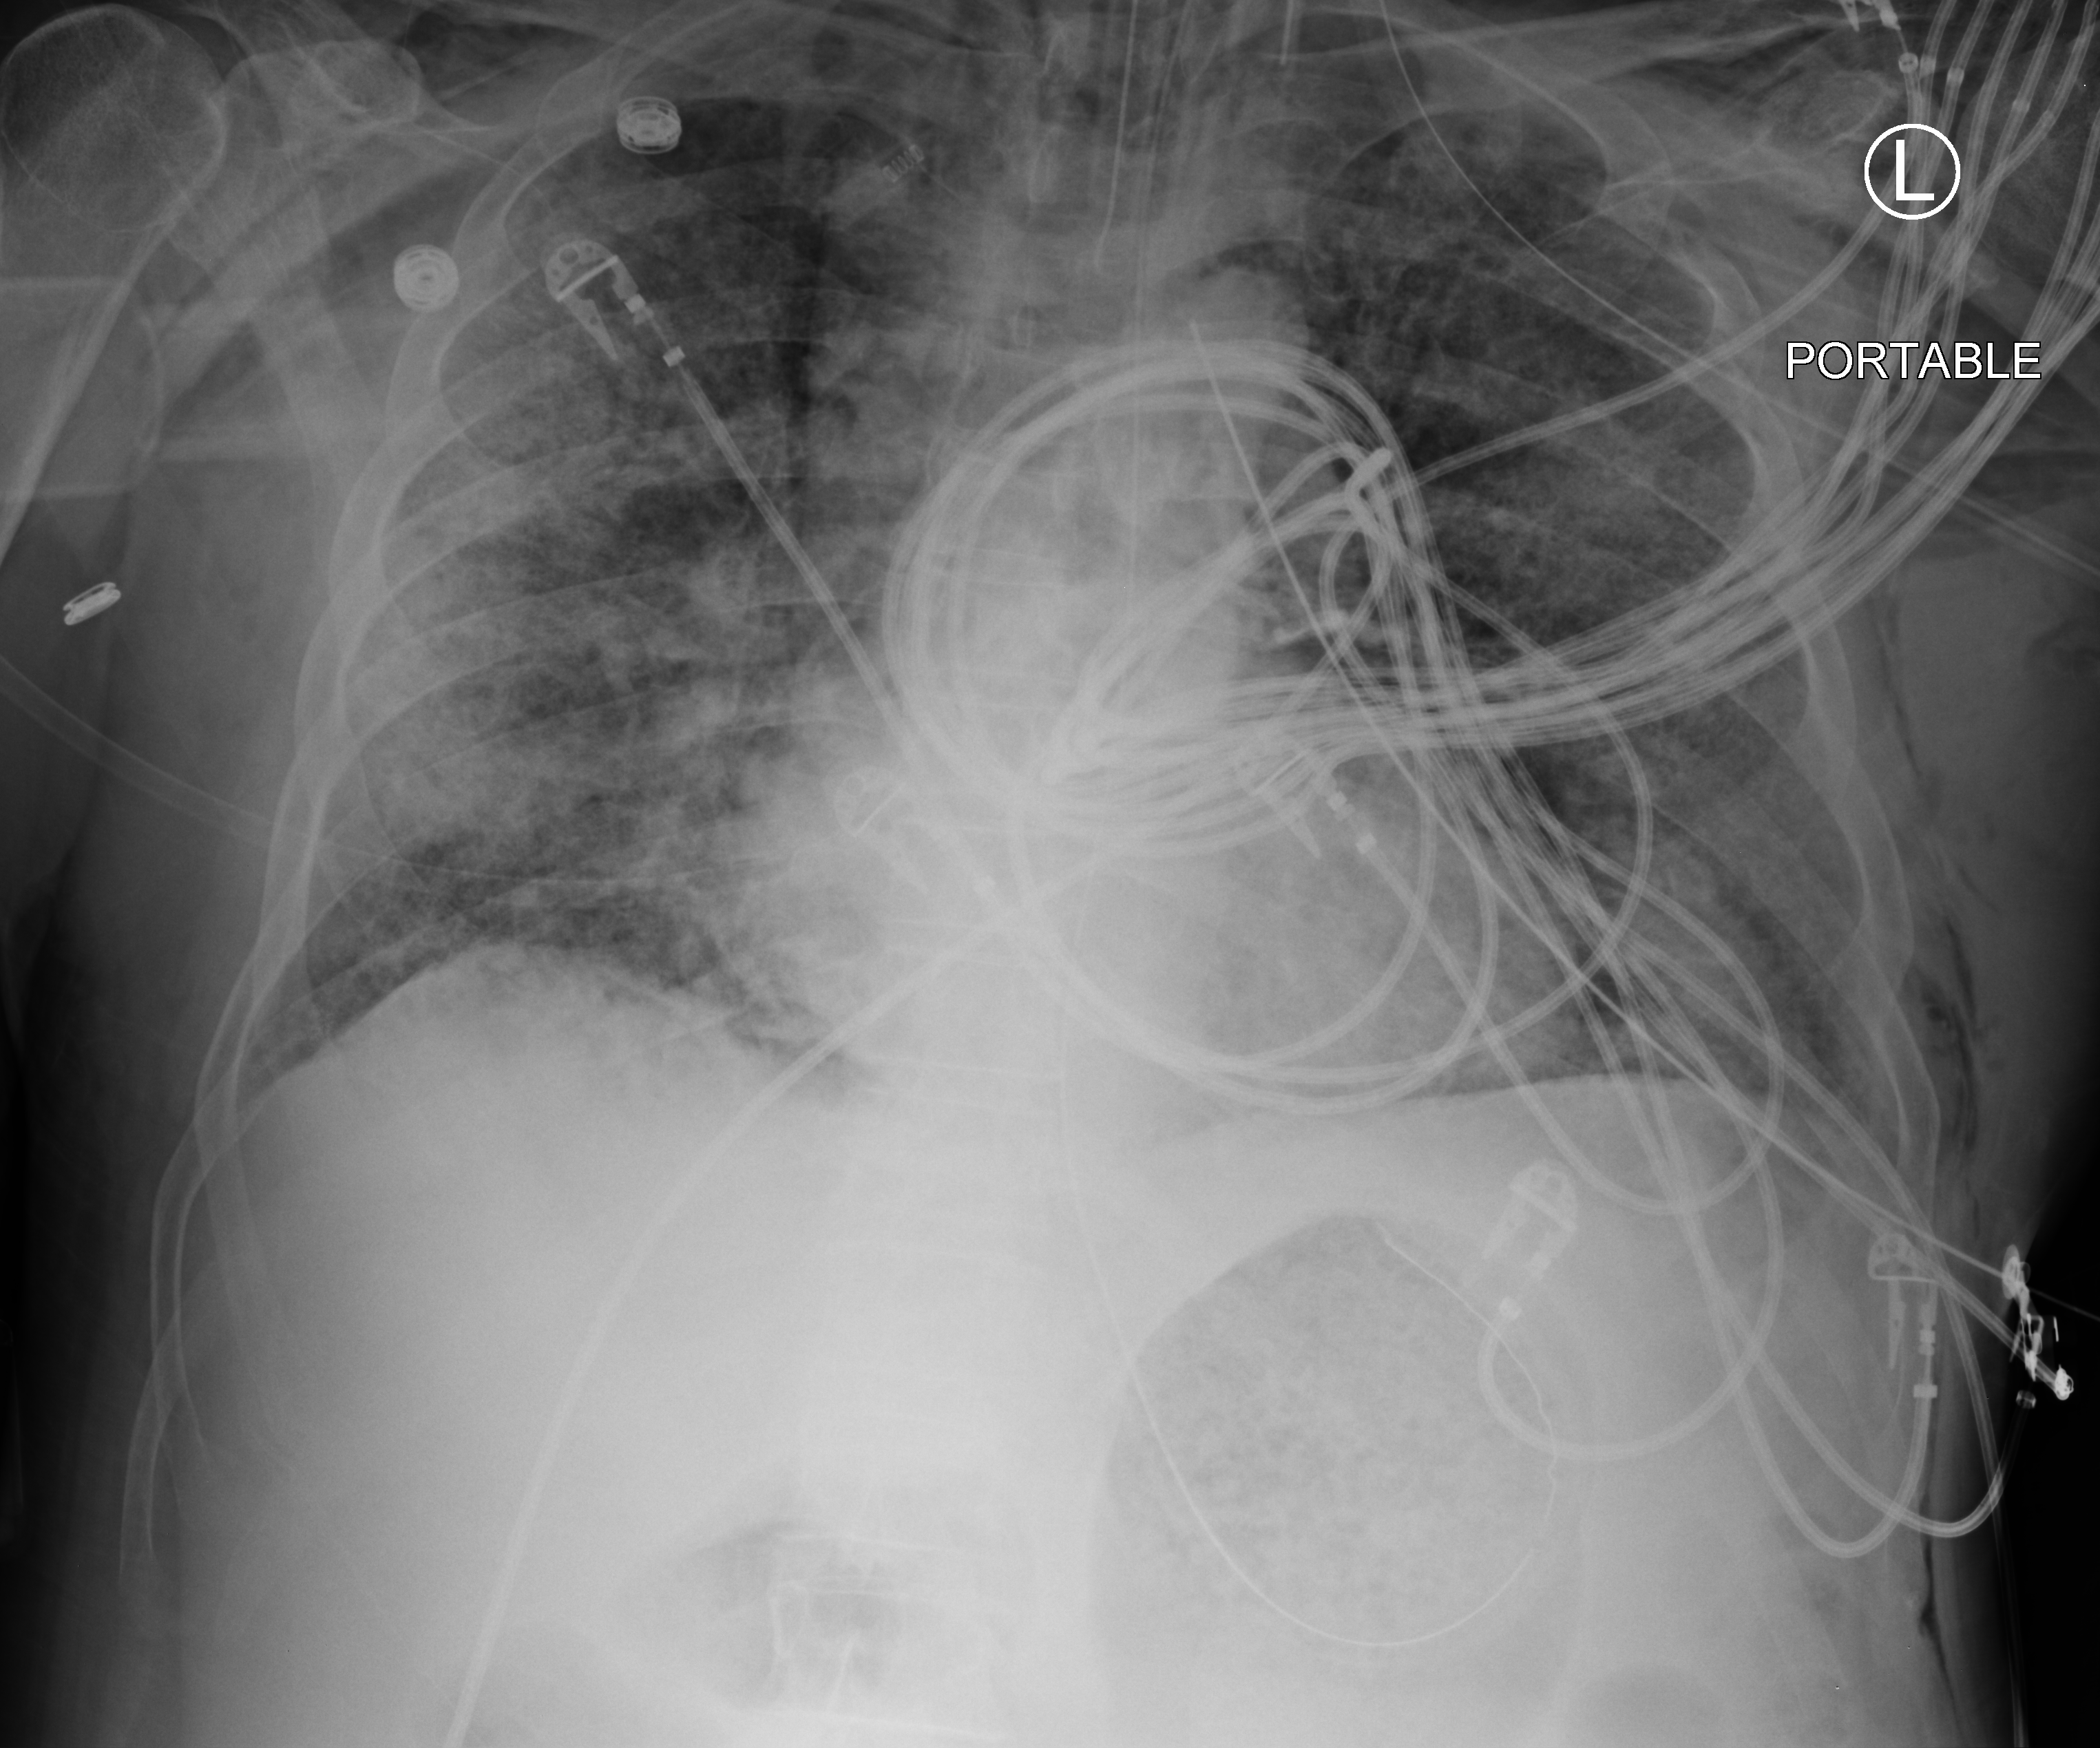
Bedside chest radiograph (computed radiography). Patient hospitalised with COVID-19; male, aged 60–74 years.
From the hospital-stay record, not from the radiograph (when in the stay this image was taken is not recorded):
- mechanically ventilated during this hospital stay: yes